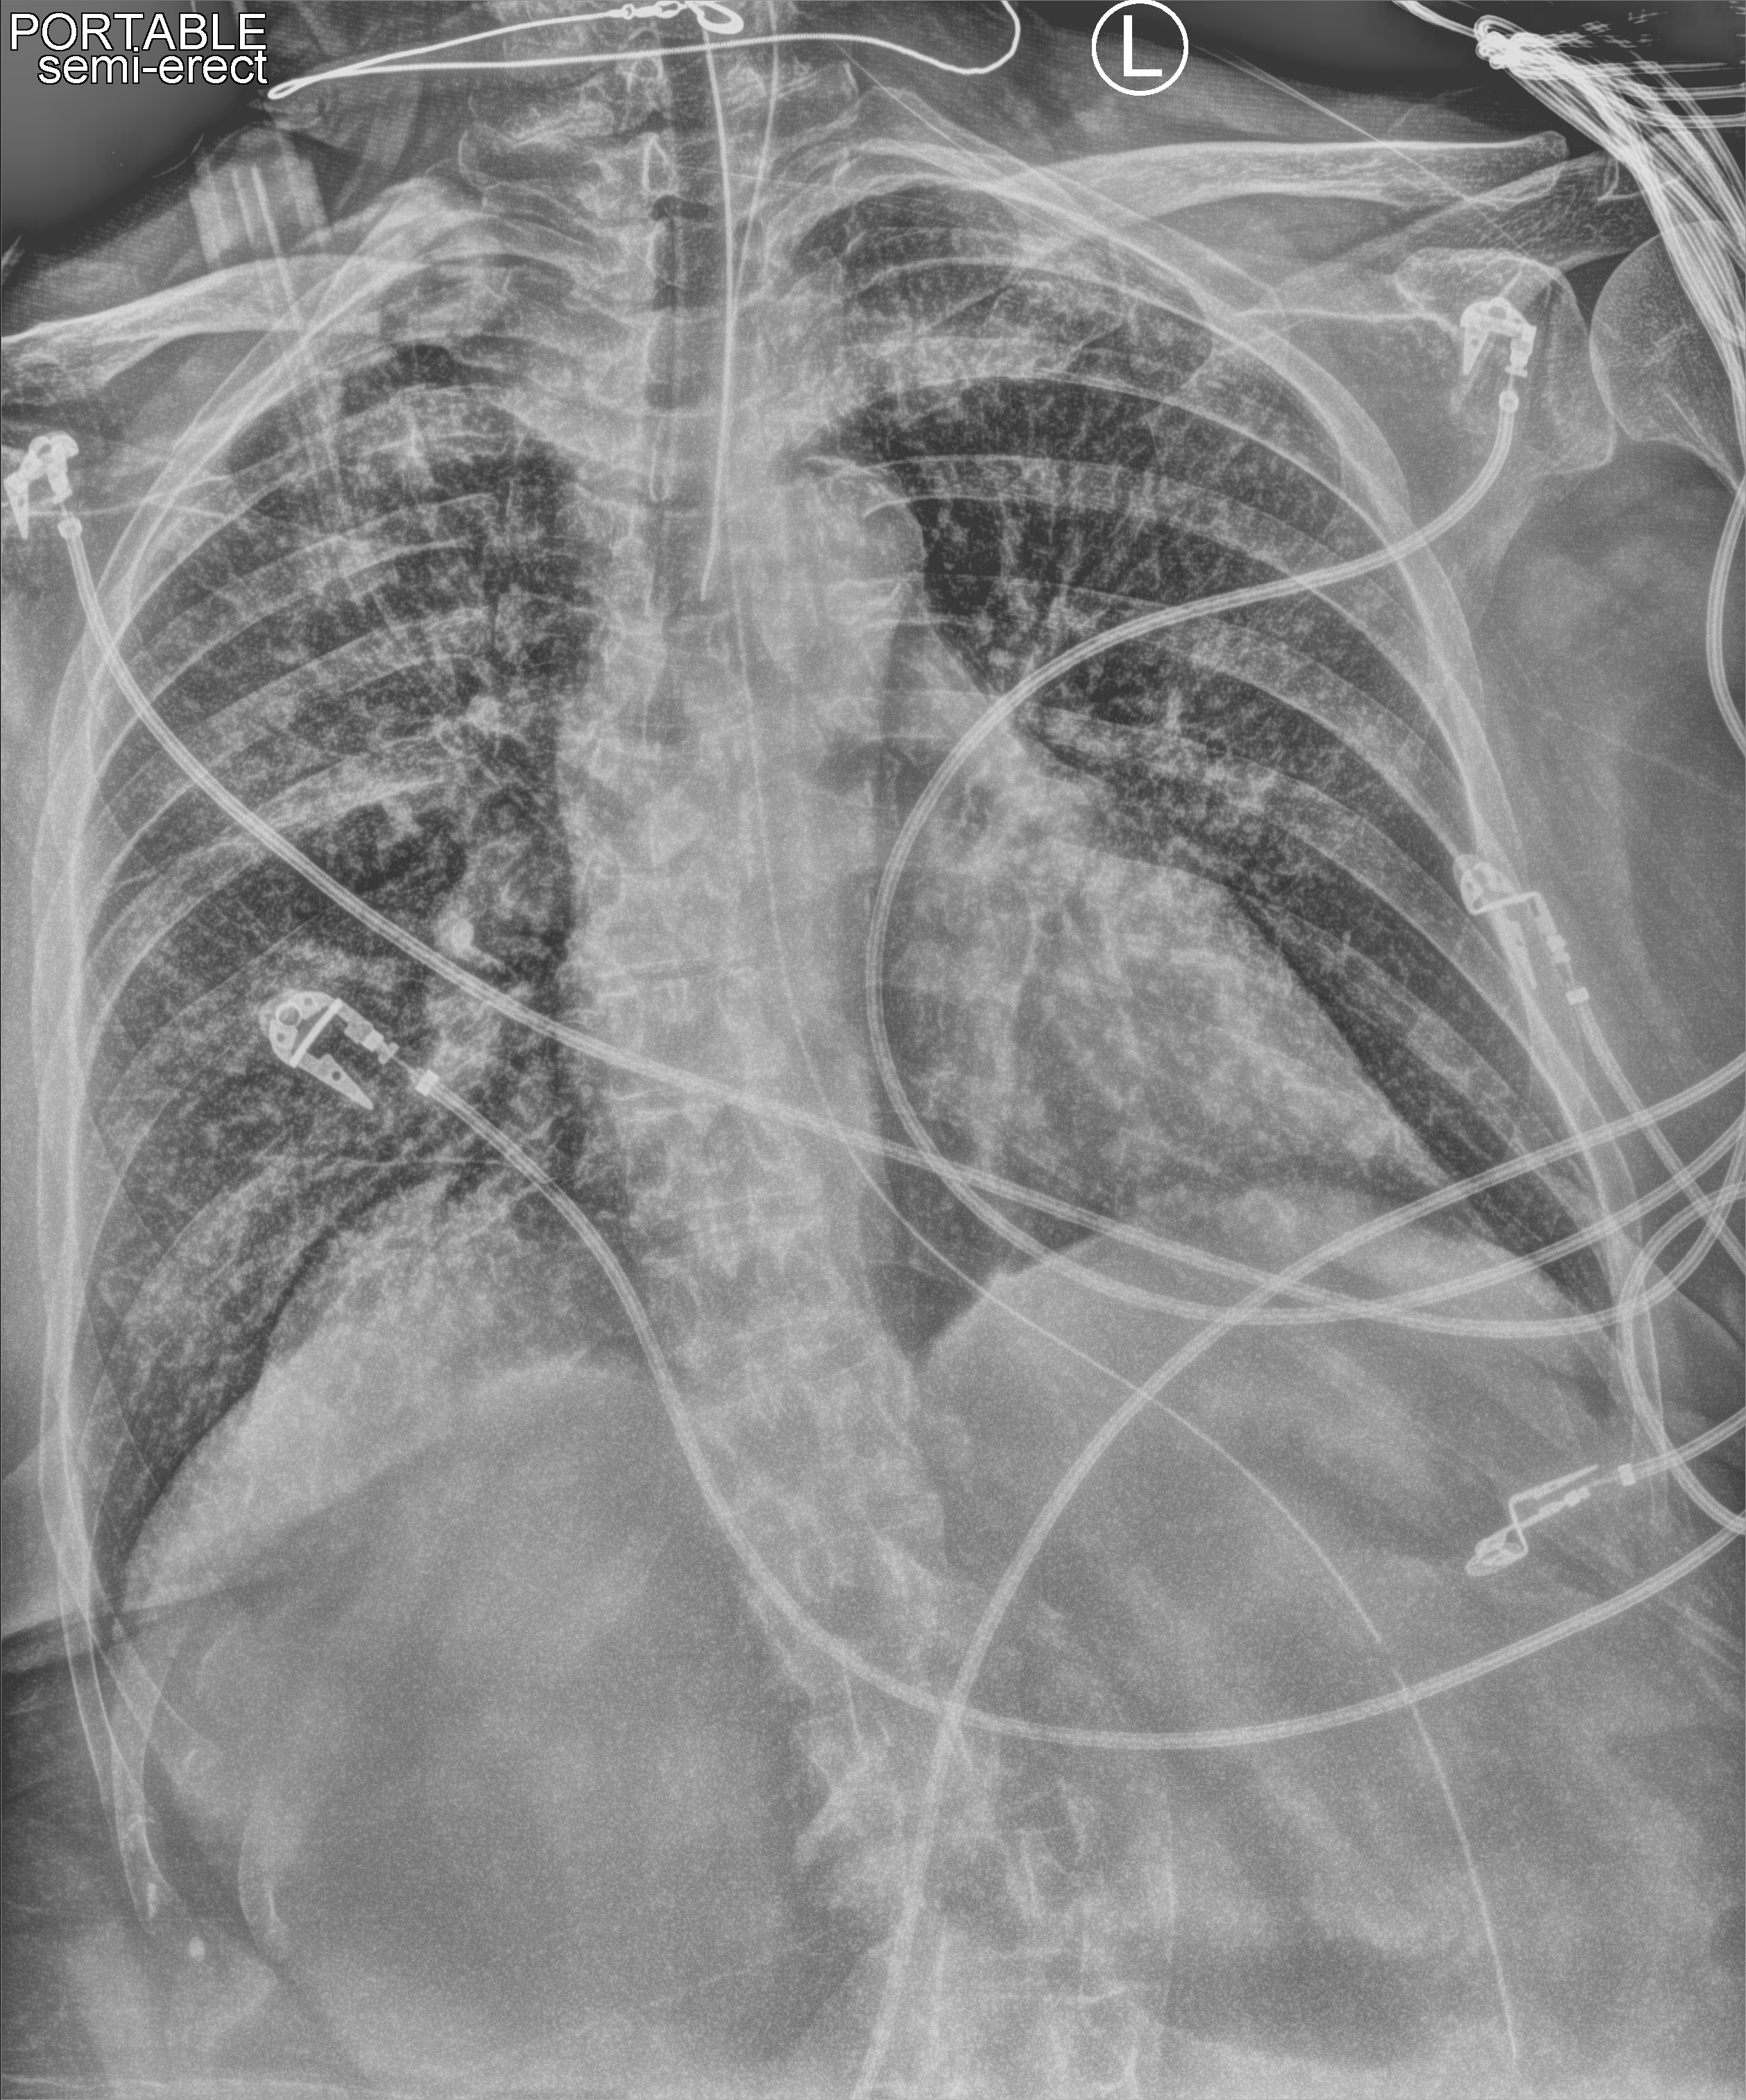
Bedside chest radiograph (computed radiography), anteroposterior (AP) projection. Female patient hospitalised with COVID-19, age 75–90 years.
From the hospital-stay record, not from the radiograph (when in the stay this image was taken is not recorded):
- admitted to intensive care during this hospital stay: yes
- other chronic lung disease (admission record): no
- mechanically ventilated during this hospital stay: yes